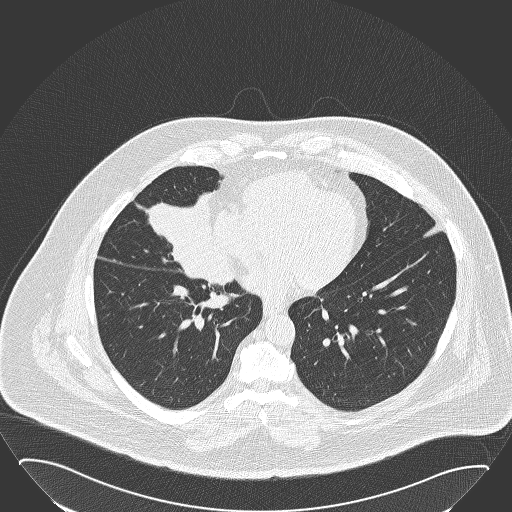
Low-dose screening chest CT, one axial slice; slice 70 of 168 in the series (ordered by position); reconstruction kernel B50f; 120 kVp; lung window (W 1500 / L -600 HU); 512 × 512 image matrix, field of view 432 × 432 mm.
Structures marked on this image (manually delineated by an expert):
- lesion 1 (tumor, hilum of right lung): bounding box [x1, y1, x2, y2] px = [143, 193, 235, 287]